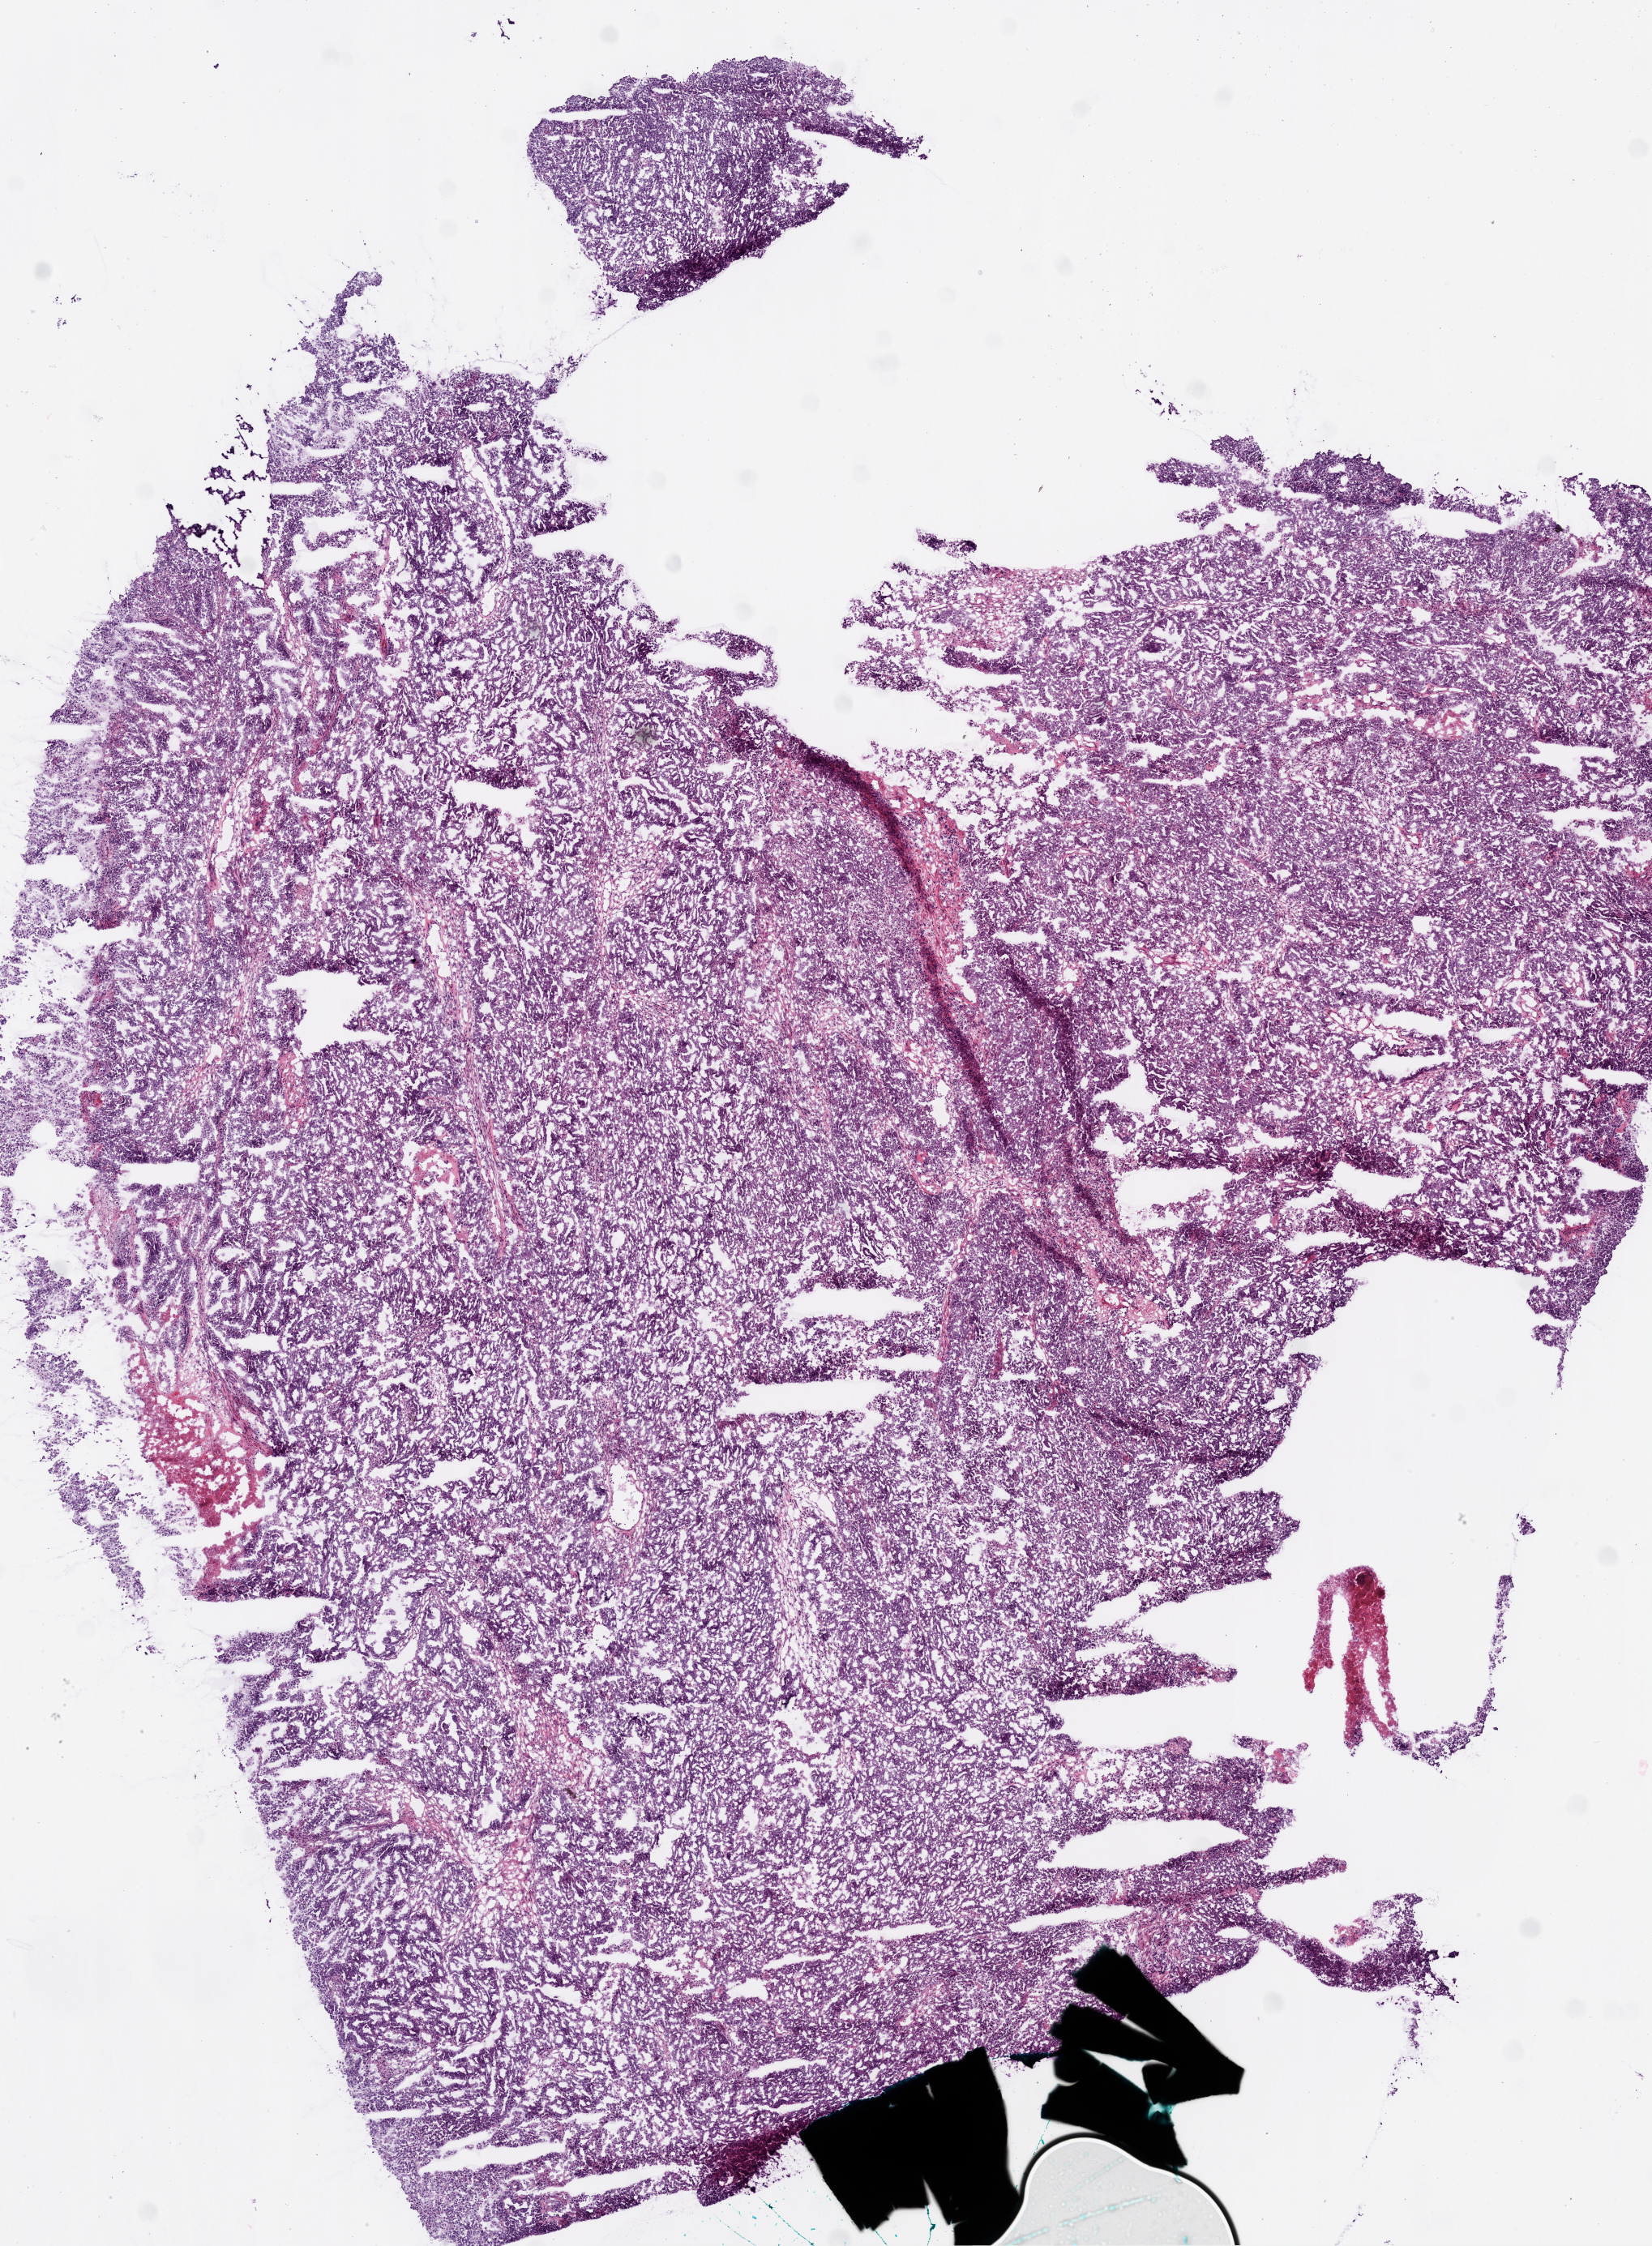
H&E whole-slide image — a low-resolution overview of the entire scanned area, about 8.2 x 11.2 mm (acquisition: 20x scan). Frozen section from the bottom of the tissue portion. Ovary, primary tumour sample. Female patient. Composition of this section per pathologist review: tumour cells 94%, tumour nuclei 99%.
Histologic diagnosis: Serous cystadenocarcinoma, NOS.